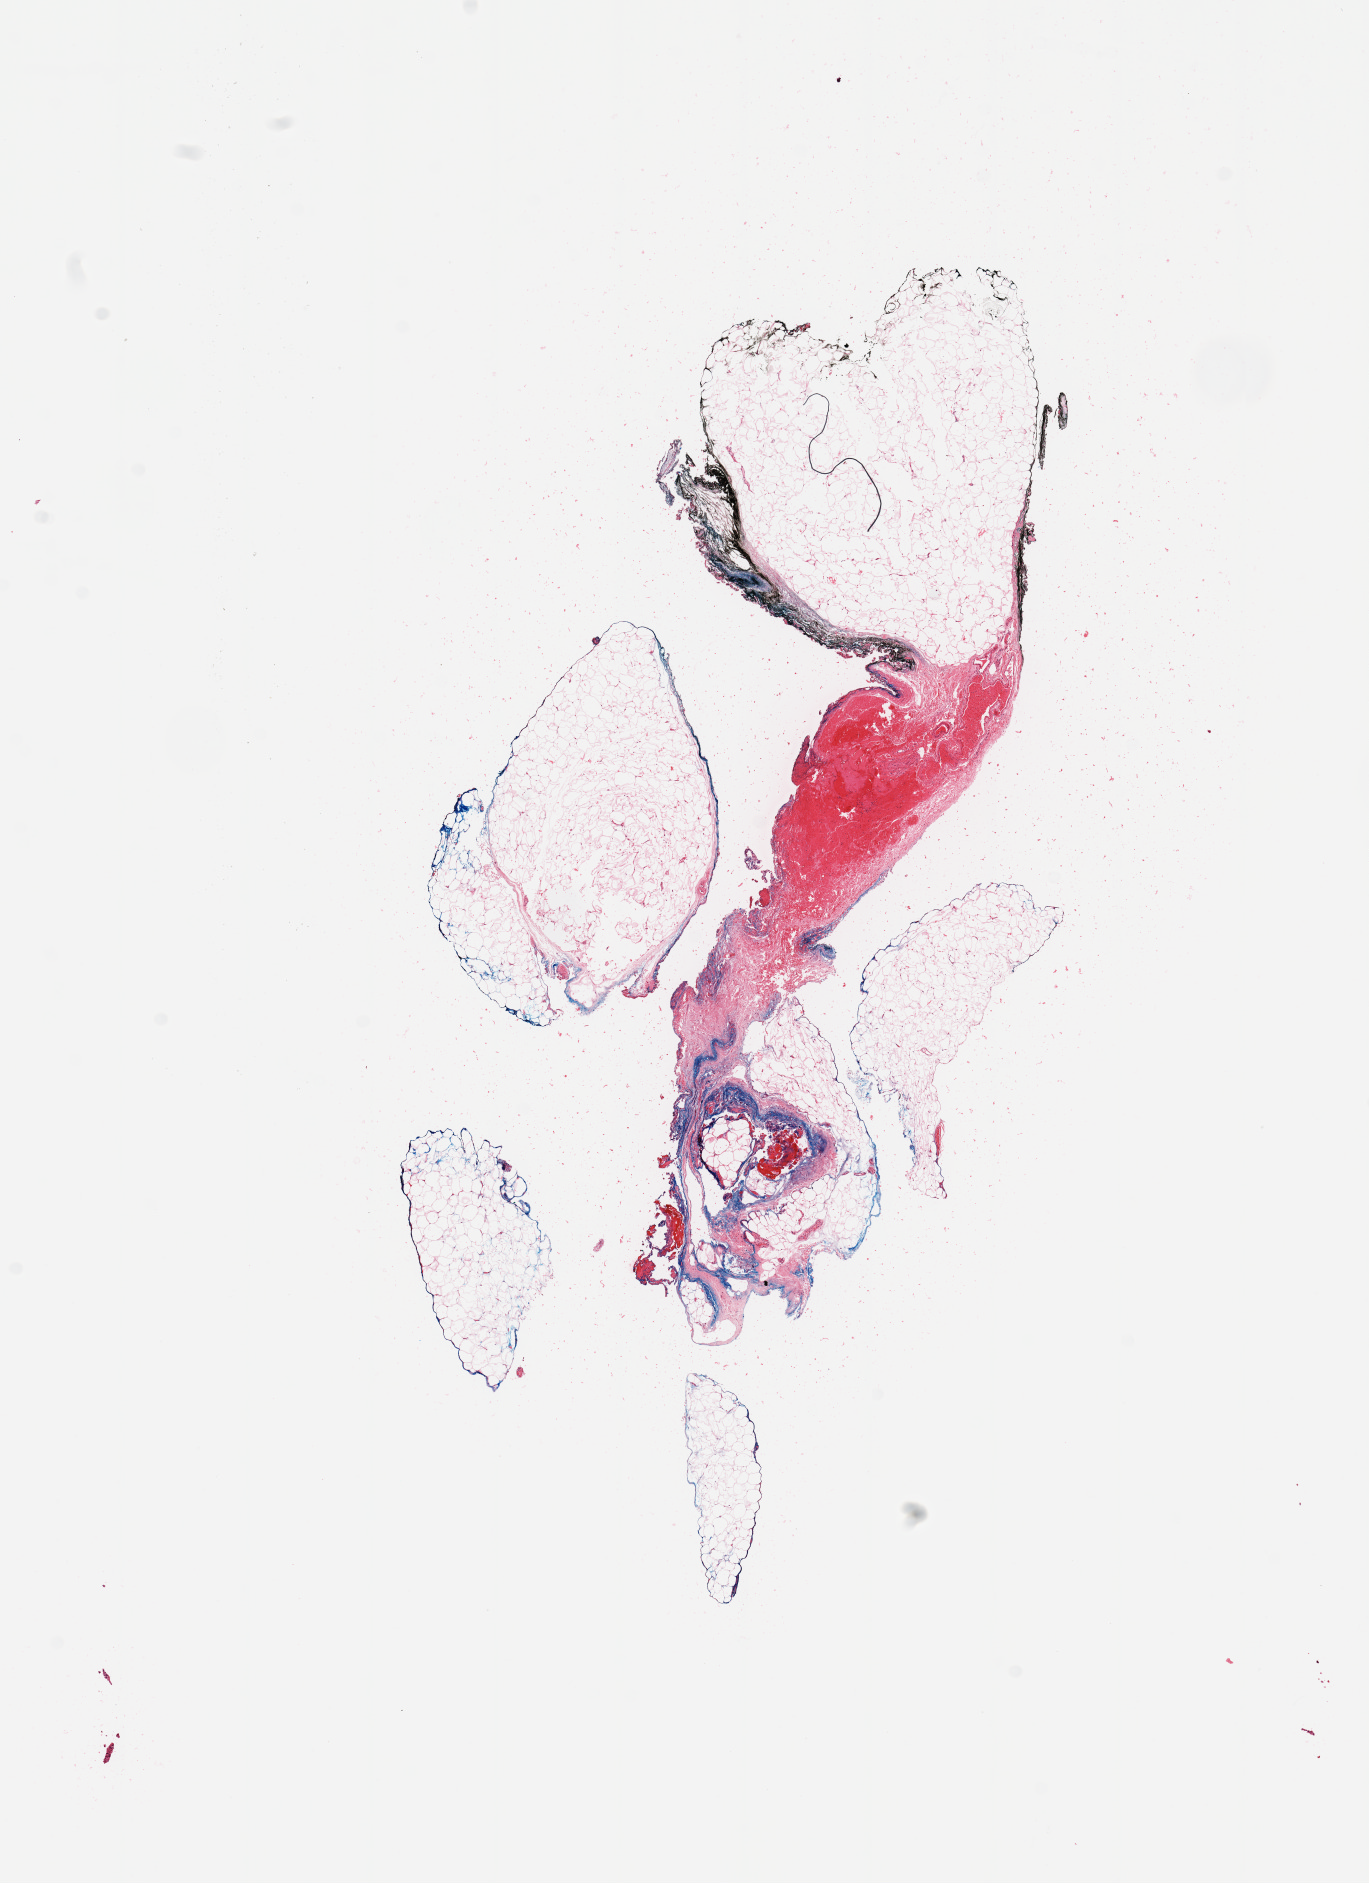
Hematoxylin and eosin (H&E) stained whole-slide image — low-resolution overview of the scanned area, about 10.8 x 14.9 mm, normal (non-tumour) tissue sample. Female patient.
This section: normal (non-tumour) tissue from the same patient. Patient diagnosis (cohort enrolment): sarcoma (site not recorded at cohort level).